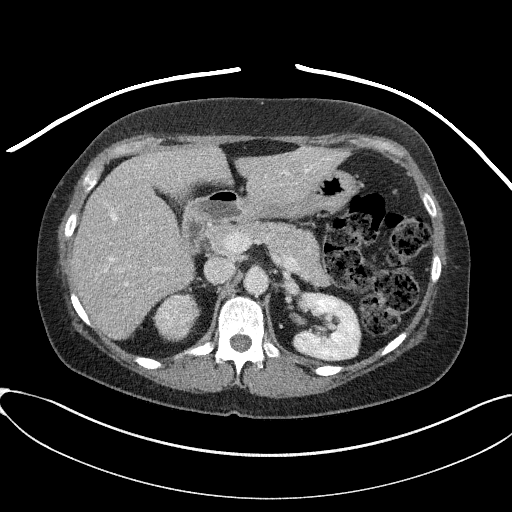
Contrast-enhanced abdominal CT, one axial slice. Position 50 of 95 along the scan axis. Intravenous contrast given. Soft-tissue window (W 400 / L 40 HU). 3 mm slice thickness. 512 × 512 image matrix. Female patient, age 46 years. From the clinical record (not read from this slice): diagnosis: adrenocortical carcinoma; tumour side: right adrenal; tumour size at pathology: 7.2 cm; Ki-67 index: 50 %; stage (as recorded): 4.
Structures marked on this image (semi-automatically segmented with operator editing):
- mass: bounding box <156,296,195,338> (left, top, right, bottom; pixels)